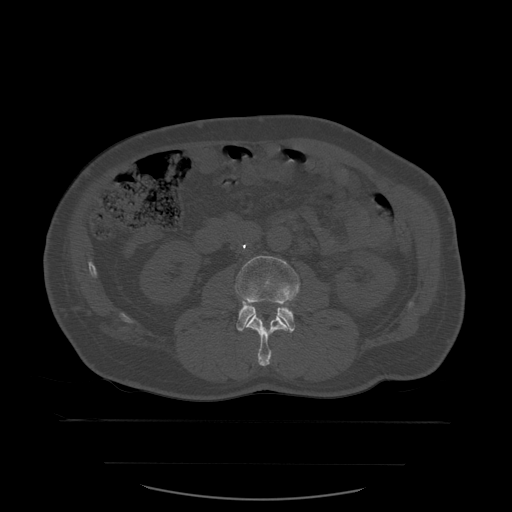
CT including the spine, one axial slice; position 203 of 590 along the scan axis; bone window (W 1800 / L 400 HU); 1.25 mm slice thickness; 512 × 512 image matrix, field of view 479 × 479 mm. Patient age 71 years. From the clinical record (not read from this slice): primary cancer: lung; vertebrae with lytic lesions (as recorded): T1, T2, L5, S1.
Structures marked on this image (semi-automatic segmentation, software-assisted and operator-edited):
- L2 vertebra: bounding box <245,311,290,367> (left, top, right, bottom; pixels)
- L3 vertebra: <235,256,301,333>